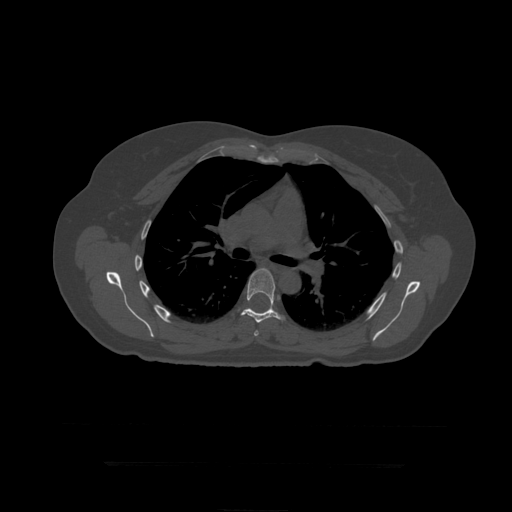
CT including the spine, one axial slice; 120 kVp; bone window (W 1800 / L 400 HU); 1.25 mm slice thickness; 512 × 512 image matrix. Patient age 41 years. Case-level facts recorded for this patient, not image findings: primary cancer: breast.
Structures marked on this image (semi-automatic segmentation, software-assisted and operator-edited):
- T6 vertebra: bounding box [x1, y1, x2, y2] px = [254, 330, 259, 336]
- T7 vertebra: [241, 268, 285, 323]